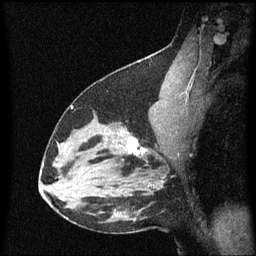
Breast MRI (dynamic contrast-enhanced), one sagittal slice. Dynamic contrast-enhanced series, image 2 of 3 at this slice position (ordered by acquisition). 1.5 T. TE 4.2 ms, TR 8.4 ms. 2 mm slice thickness. 256 × 256 image matrix, field of view 200 × 200 mm. Patient: female, 38 years. Case-level facts recorded for this patient, not image findings: setting: breast cancer imaged before/during neoadjuvant chemotherapy; receptor status: HR-positive, HER2-negative.
Structures marked on this image (semi-automatically segmented with operator editing):
- analysis volume of interest (the breast-tissue region the enhancement analysis was run in; not a lesion): box from (x=122, y=126) to (x=154, y=163) px
- tumour enhancement mask (voxels above the 70 % enhancement threshold inside the analysis volume of interest): (x=127, y=132)–(x=147, y=155)